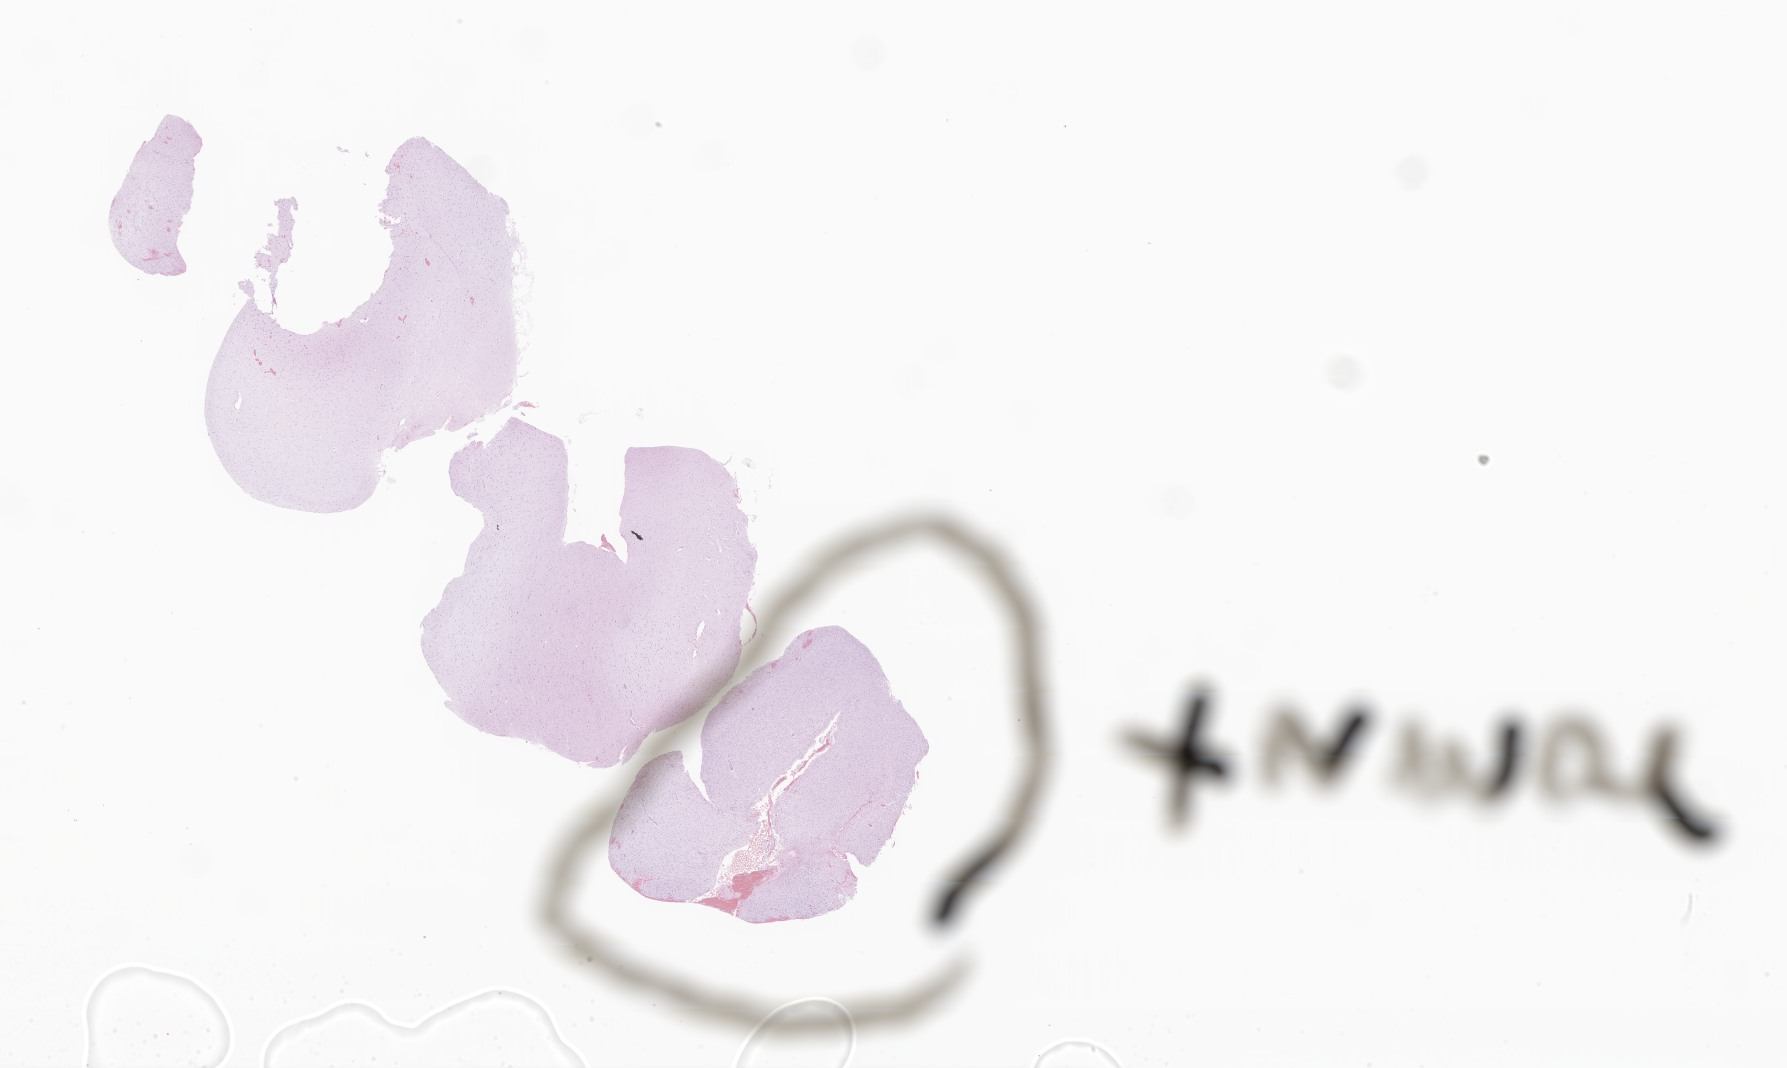
H&E whole-slide image of tumor tissue from the brain, low-resolution overview of the scanned area, about 30.1 x 18.0 mm. Formalin-fixed paraffin-embedded section. Male patient, age 211 months (17 years 7 months).
Diagnosis (ICD-O-3 morphology term): Glioma, malignant.